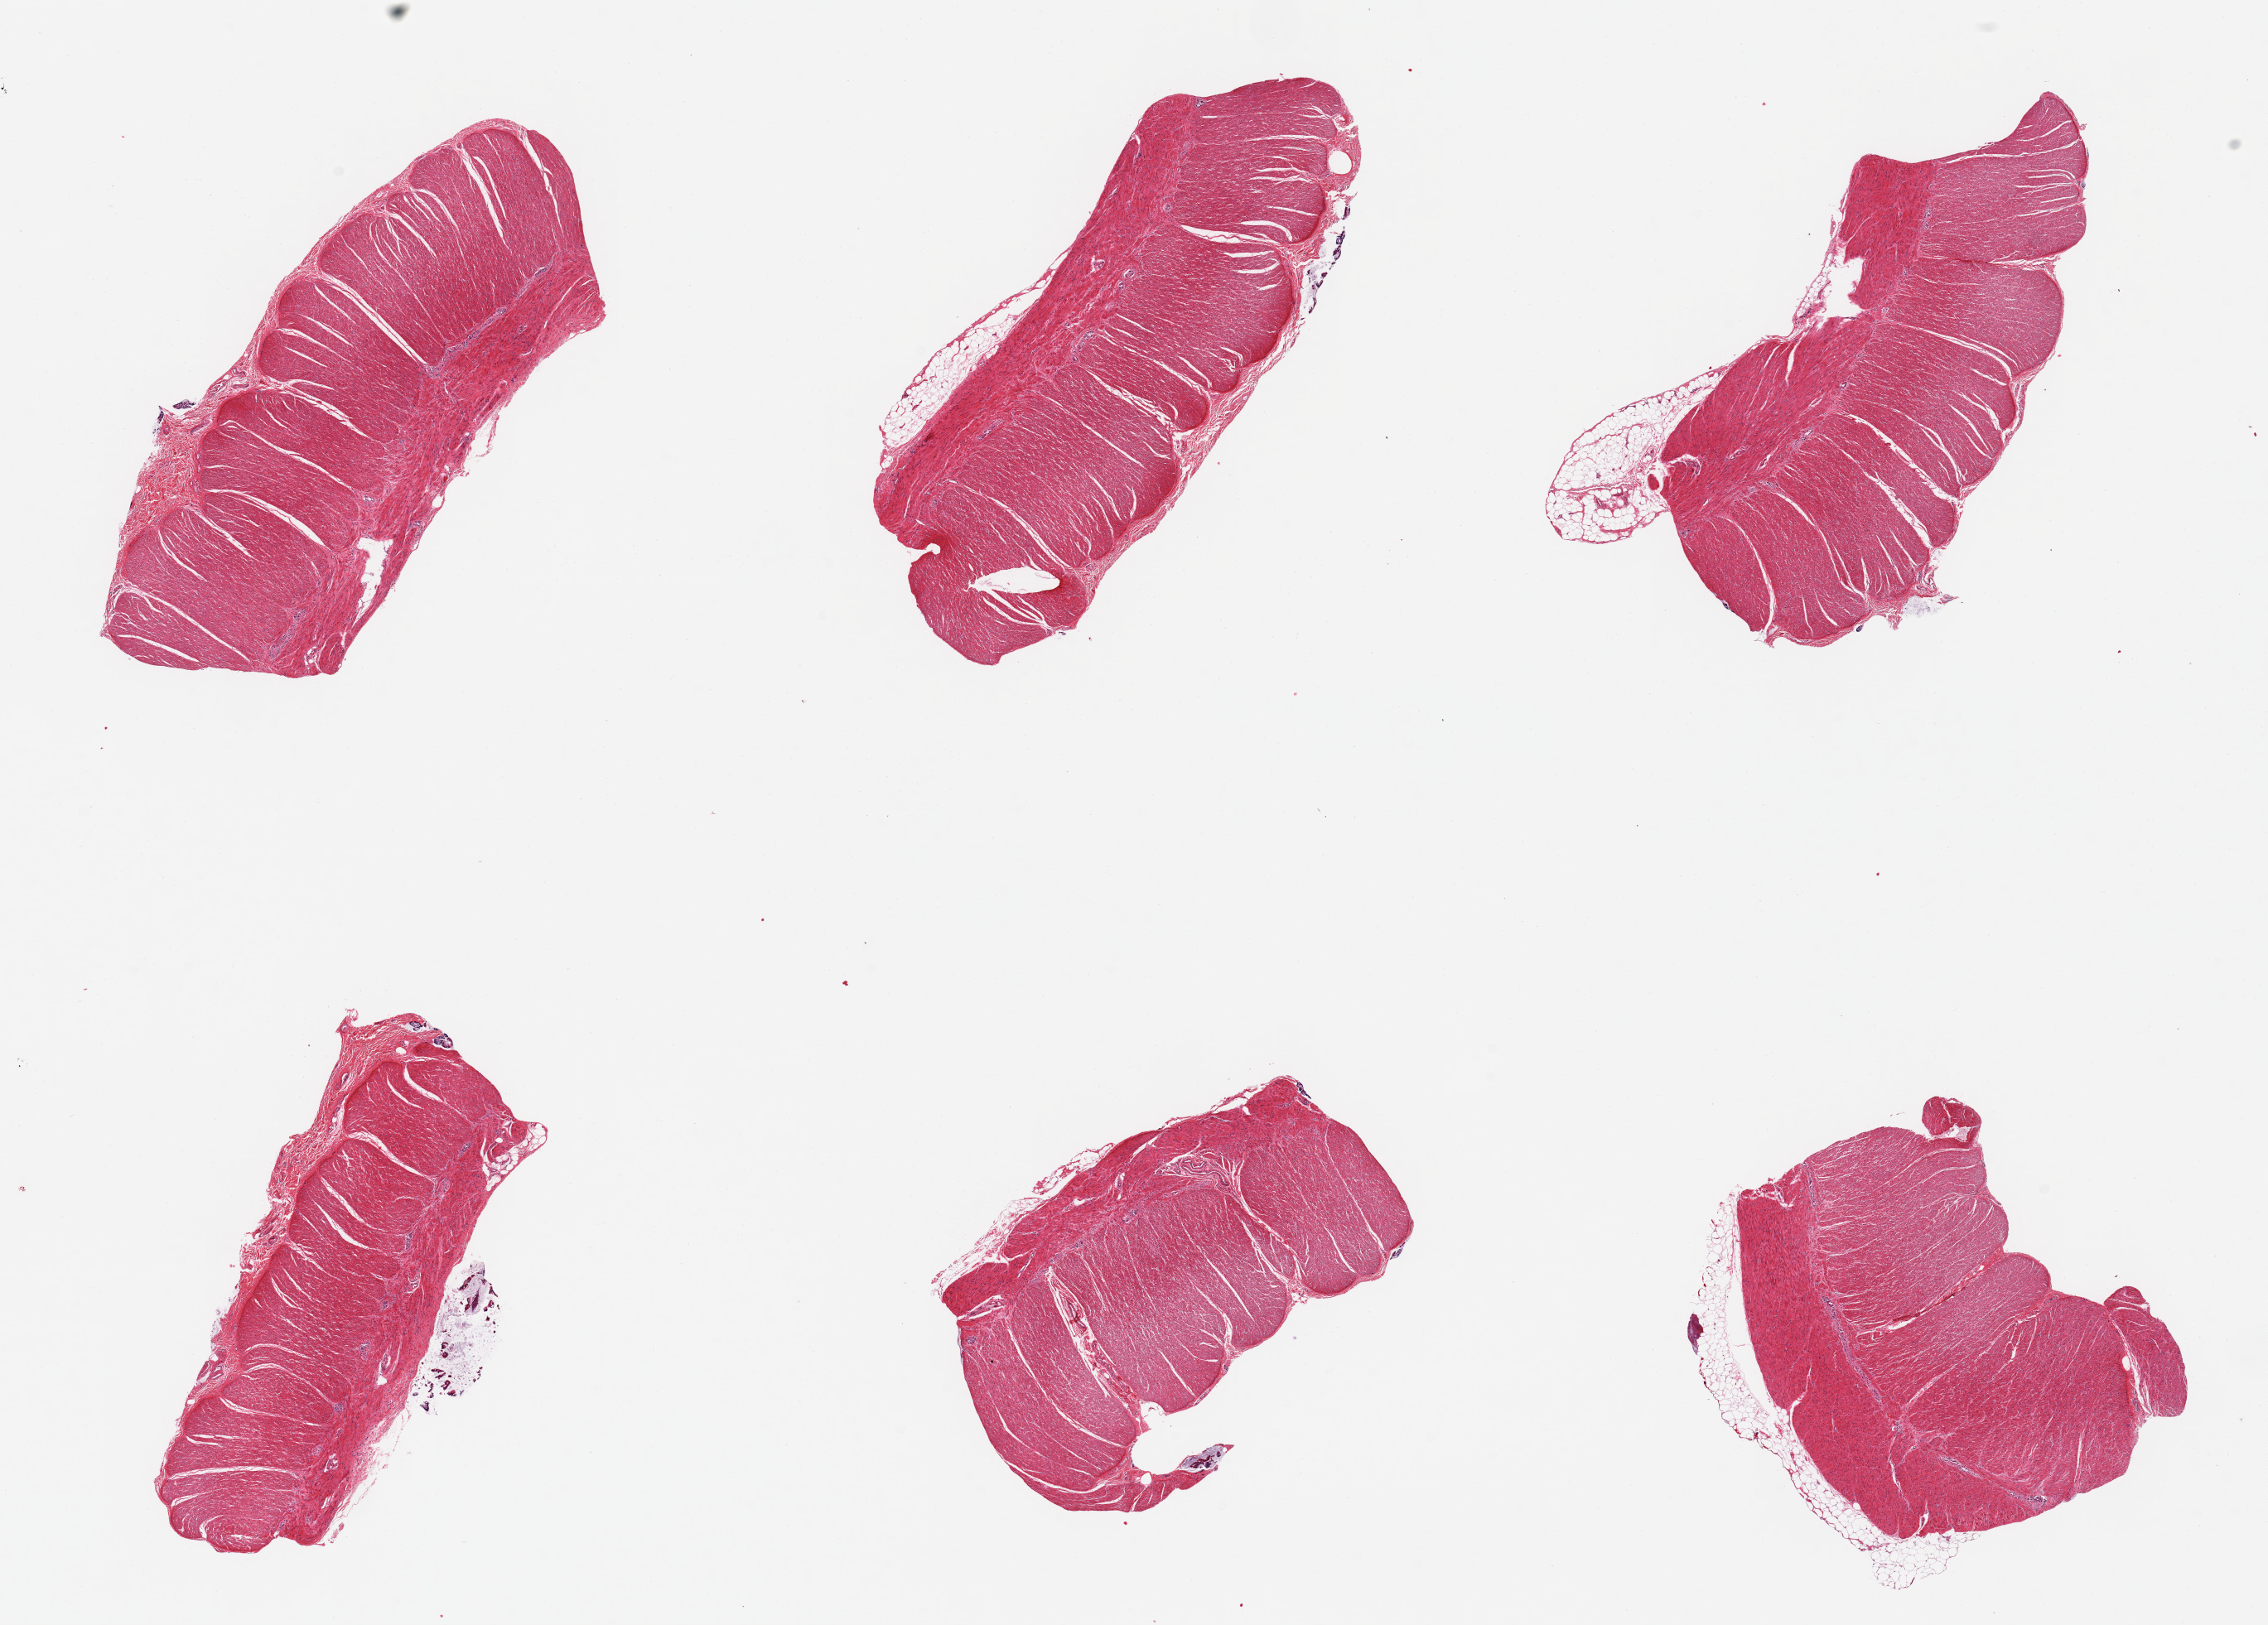
Digitized haematoxylin and eosin-stained section — low-resolution overview of the scanned area, about 21.7 x 15.5 mm (acquisition: 20x scan), PAXgene-fixed, paraffin-embedded tissue, sampled site (target tissue): sigmoid colon, donor tissue sample. Male donor.
Reviewer comment on this tissue sample: 6 pieces; target muscularis.